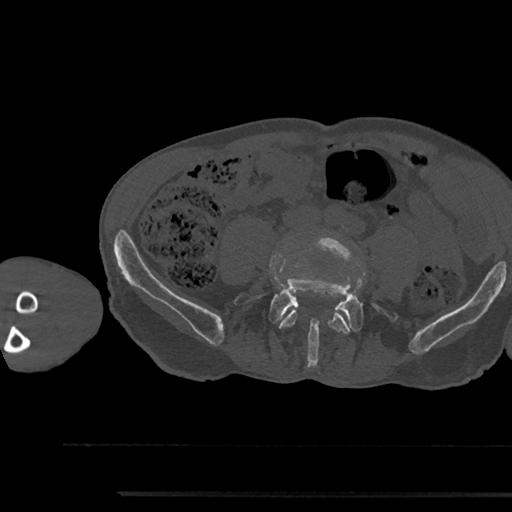
CT including the spine, one axial slice; position 373 of 797 along the scan axis; reconstruction kernel Br40s/3; bone window (W 1800 / L 400 HU); 0.5 mm slice thickness; 512 × 512 image matrix, field of view 367 × 367 mm. Male patient, age 79 years. Case-level facts recorded for this patient, not image findings: primary cancer: prostate.
Structures marked on this image (semi-automatically segmented with operator editing):
- L4 vertebra: box from (x=279, y=236) to (x=364, y=334) px
- L5 vertebra: (x=235, y=268)–(x=399, y=366)